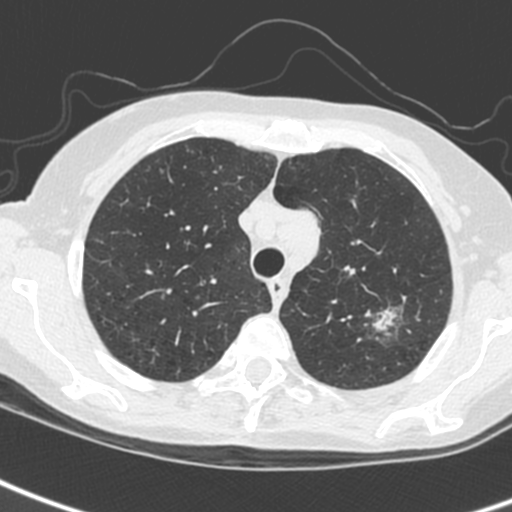
Low-dose screening chest CT, one axial slice; position 202 of 242 along the scan axis; lung window (W 1500 / L -600 HU); 1.3 mm slice thickness; 512 × 512 image matrix, field of view 284 × 284 mm.
Structures marked on this image (outlined manually by an expert reader):
- lesion 1 (tumor, upper lobe of left lung): bounding box [x1, y1, x2, y2] px = [374, 309, 396, 330]
- lesion 3 (tumor, upper lobe of left lung): [299, 210, 320, 257]